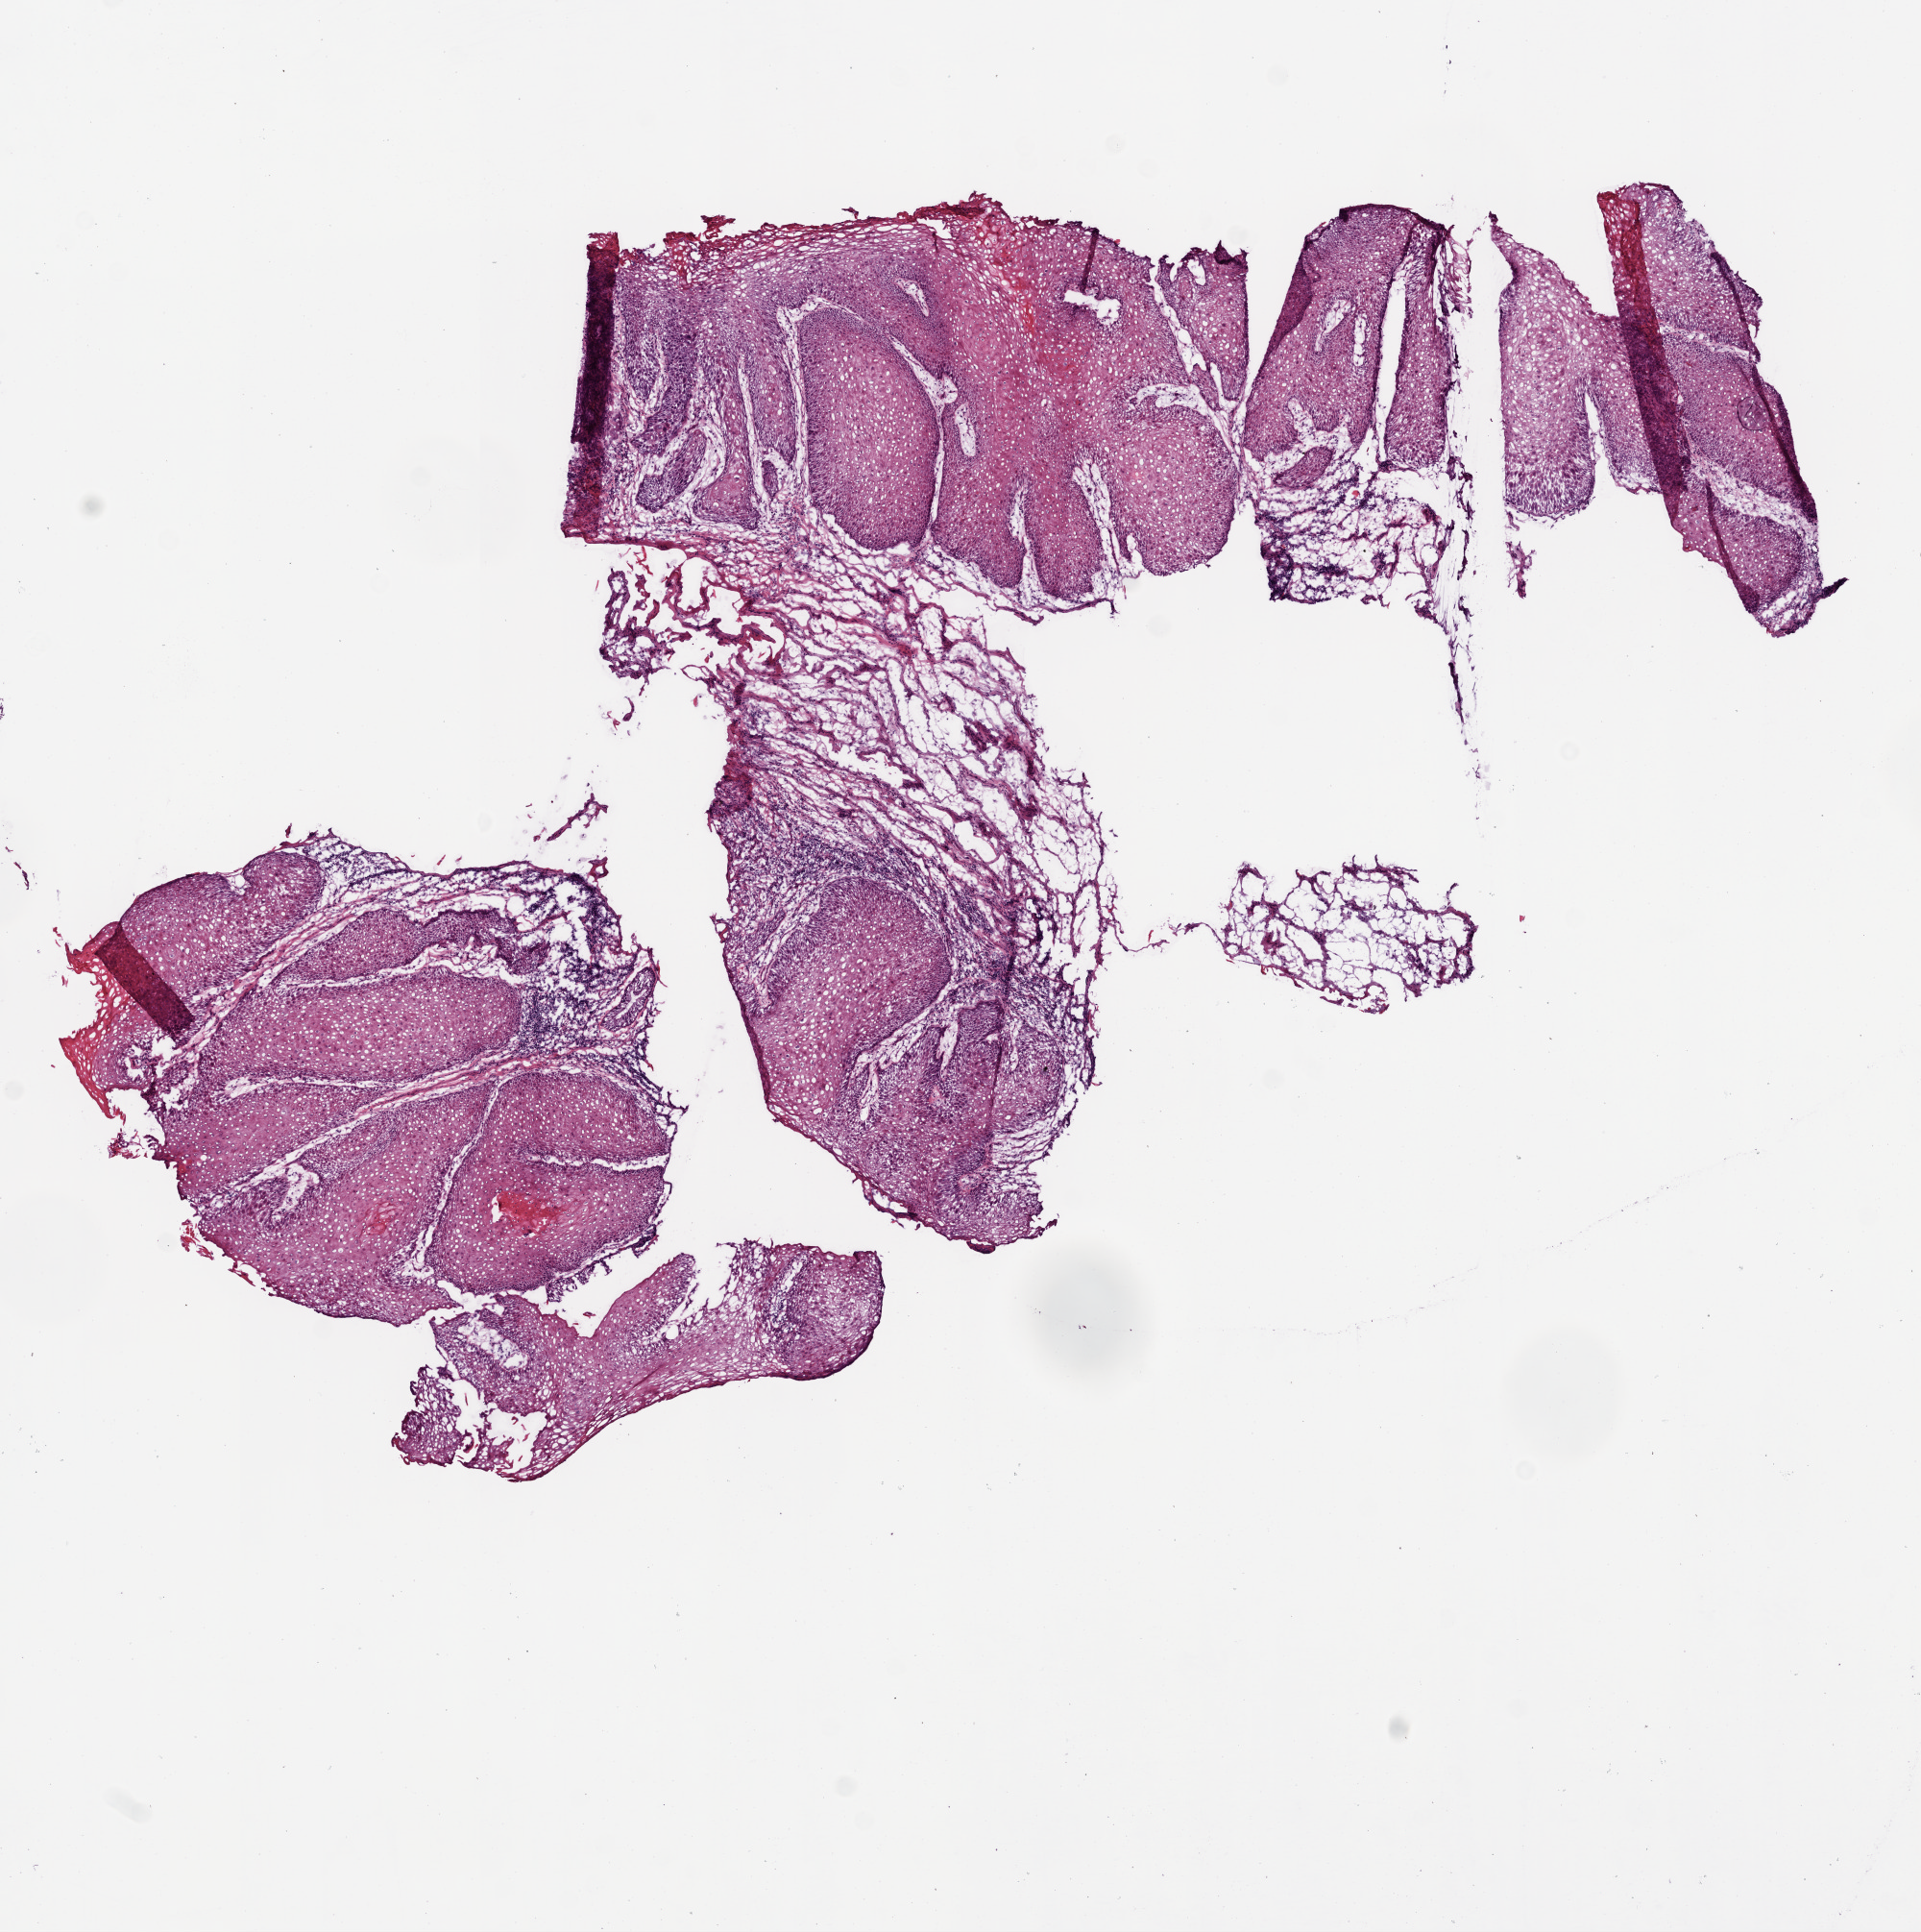
Whole-slide histology image, H&E-stained, whole scanned area (about 8.0 x 8.1 mm) shown as a low-resolution overview, frozen section from the top of the tissue portion, primary tumour sample from the head and neck. Female, age 61 years at initial diagnosis. Histologic grade: G1 (well differentiated). Composition of this section per pathologist review: tumour cells 80%, tumour nuclei 80%, normal cells 0%, stromal cells 20%, necrosis 0%.
- AJCC pathologic stage: II (7th edition)
- pathologic diagnosis: Squamous cell carcinoma, NOS (larynx, NOS)